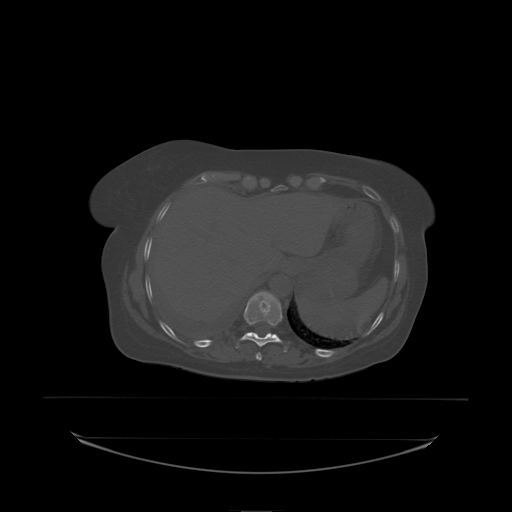
CT including the spine, one axial slice. Position 113 of 242 along the scan axis. Bone window (W 1800 / L 400 HU). 2.5 mm slice thickness. 512 × 512 image matrix, field of view 500 × 500 mm. Female patient, age 53 years. From the clinical record (not read from this slice): primary cancer: lung.
Outlined on this slice (semi-automatically segmented with operator editing):
- T10 vertebra: bounding box (x1, y1, x2, y2) in pixels: (244, 292, 283, 338)